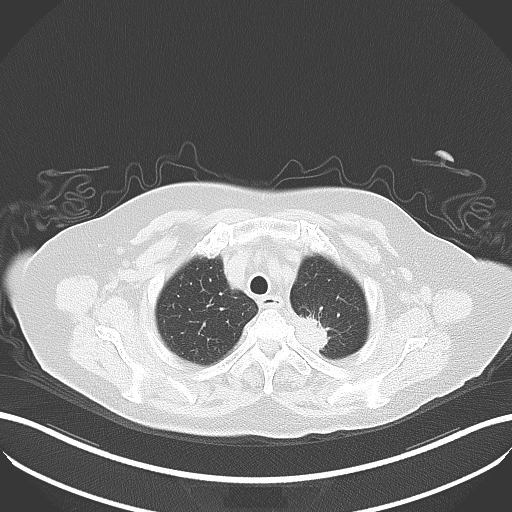
Chest CT, one axial slice. Slice 41 of 50 in the series (ordered by position). Reconstruction kernel B80f. 100 kVp. Lung window (W 1500 / L -600 HU). 5 mm slice thickness. 512 × 512 image matrix, field of view 400 × 400 mm. Patient: female, 81 years. From the clinical record (not read from this slice): clinical TNM (as recorded): T2a N0 M0.
Structures marked on this image (rectangle marked by the reading radiologist):
- lung tumour (recorded histology: adenocarcinoma): box from (x=292, y=306) to (x=336, y=353) px